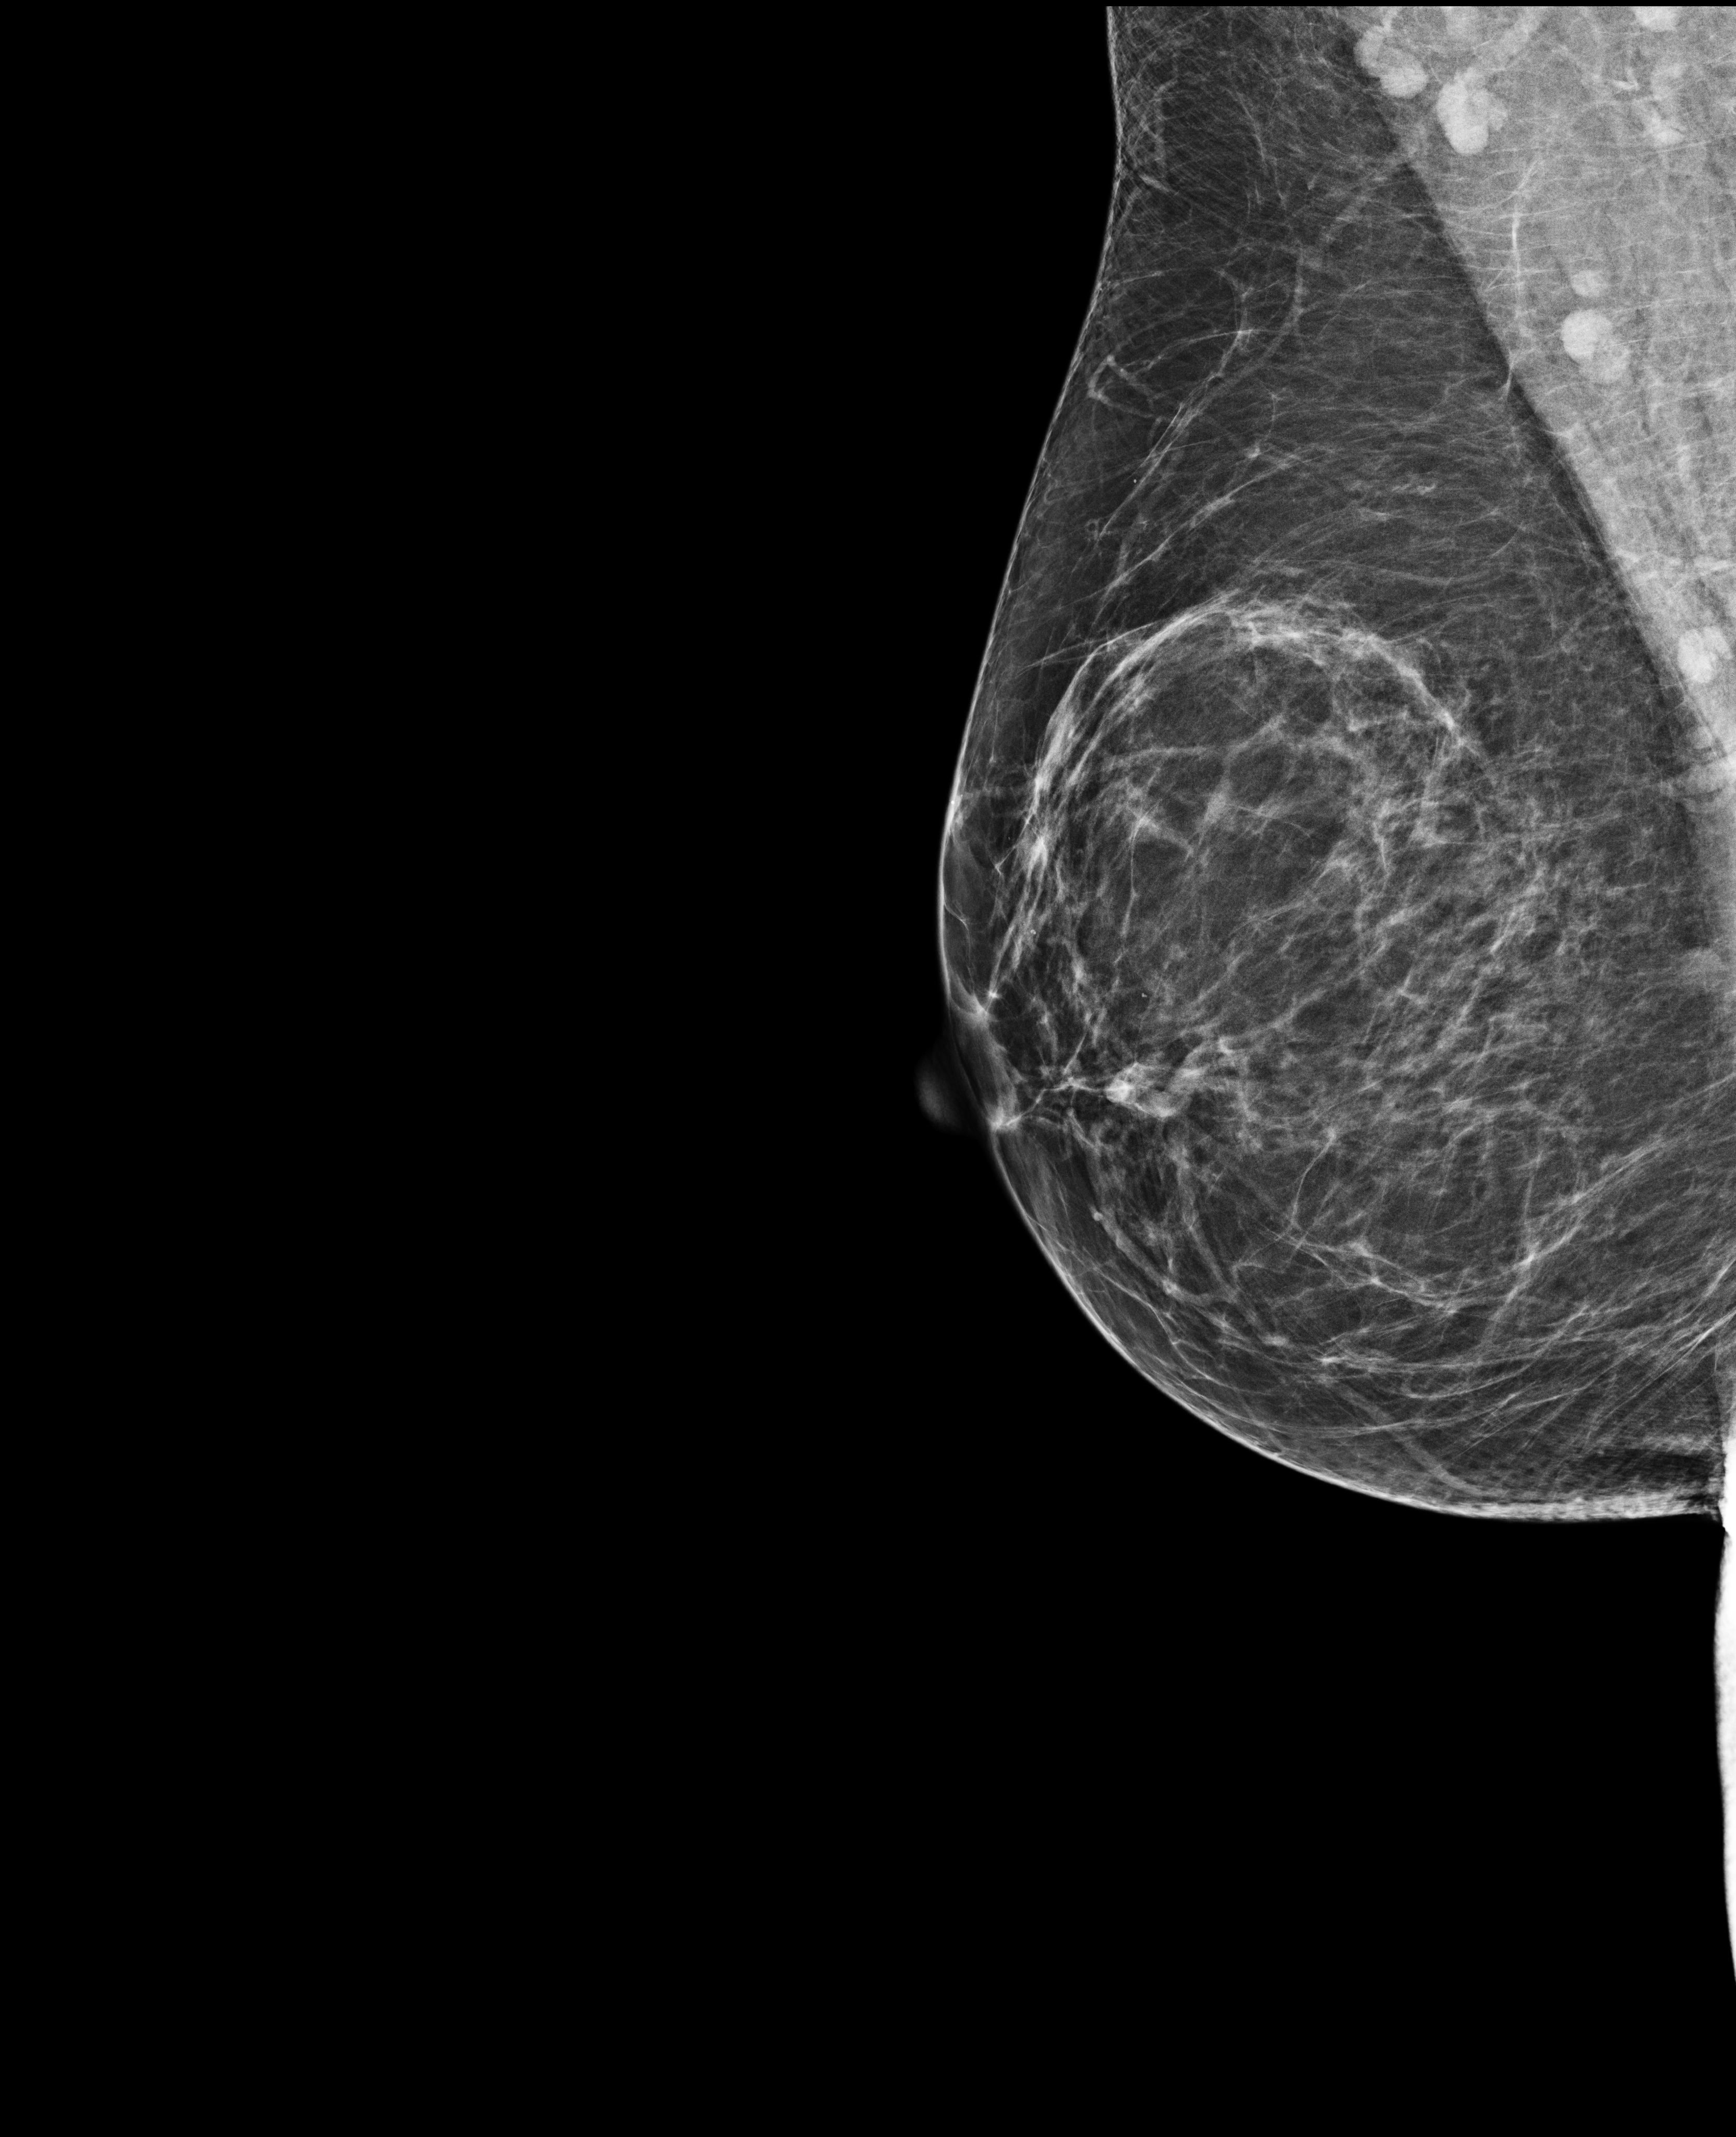
Full-field digital mammogram (FFDM); right breast; medio-lateral oblique projection; annual screening mammography examination. Patient: female, 54 years.
Final BI-RADS assessment for this screening round (tomosynthesis exam, both breasts): category 2.